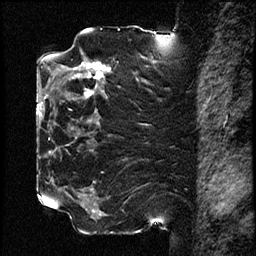
Breast MRI (dynamic contrast-enhanced), one sagittal slice. Slice 43 of 78 in the series (ordered by position). Dynamic contrast-enhanced study with each time point stored as its own series, time point 2 of 3 at this slice position (early post-contrast, ordered by acquisition time). 1.5 T. TE 4.2 ms, TR 17.6 ms. 256 × 256 image matrix, field of view 200 × 200 mm. Female patient, age 42 years. From the clinical record (not read from this slice): setting: breast cancer imaged before/during neoadjuvant chemotherapy; receptor status: HER2-positive.
Annotated regions visible in this slice (semi-automatic segmentation, software-assisted and operator-edited):
- analysis volume of interest (the breast-tissue region the enhancement analysis was run in; not a lesion): box from (x=50, y=48) to (x=121, y=129) px
- tumour enhancement mask (voxels above the 100 % enhancement threshold inside the analysis volume of interest): (x=72, y=62)–(x=111, y=96)